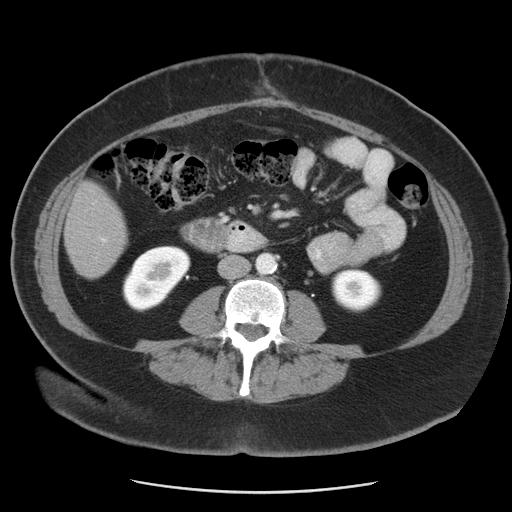
Contrast-enhanced abdominal CT, one axial slice. Slice 8 of 55 in the series (ordered by position). 120 kVp. Intravenous contrast given. Soft-tissue window (W 400 / L 40 HU). 5 mm slice thickness. 512 × 512 image matrix, field of view 380 × 380 mm. Female patient, age 52 years. Case-level facts recorded for this patient, not image findings: diagnosis: colorectal cancer liver metastases, imaged before liver resection; multiple liver metastases: yes; largest metastasis: 2.5 cm; disease in both lobes: yes.
Structures marked on this image (manually delineated by an expert):
- liver: bounding box (x1, y1, x2, y2) in pixels: (64, 181, 128, 279)
- planned liver remnant (the part of the liver to remain after resection): (64, 197, 126, 278)
- portal vein (with intrahepatic branches): (92, 200, 109, 245)